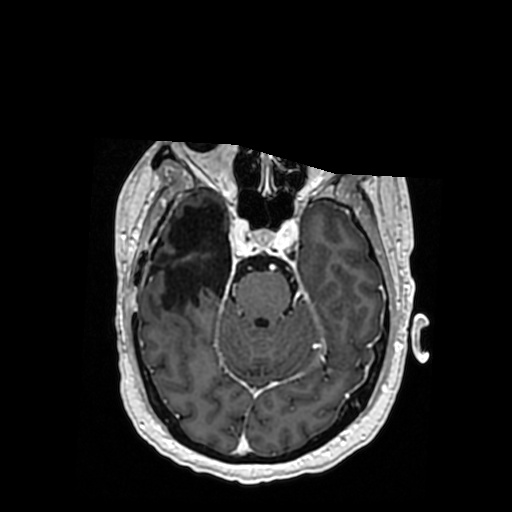
Brain MRI from a brain-tumour surgery series, one axial slice; position 232 of 364 along the scan axis; T1-weighted post-contrast; 0.5 mm slice thickness; 512 × 512 image matrix. From the clinical record (not read from this slice): histopathology: Oligodendroglioma; WHO grade: 3; IDH mutation: yes; tumour location: Right Posterior Temporal Inferior Parietal.
Outlined on this slice (manually delineated by an expert):
- previous resection cavity: box from (x=159, y=205) to (x=231, y=309) px